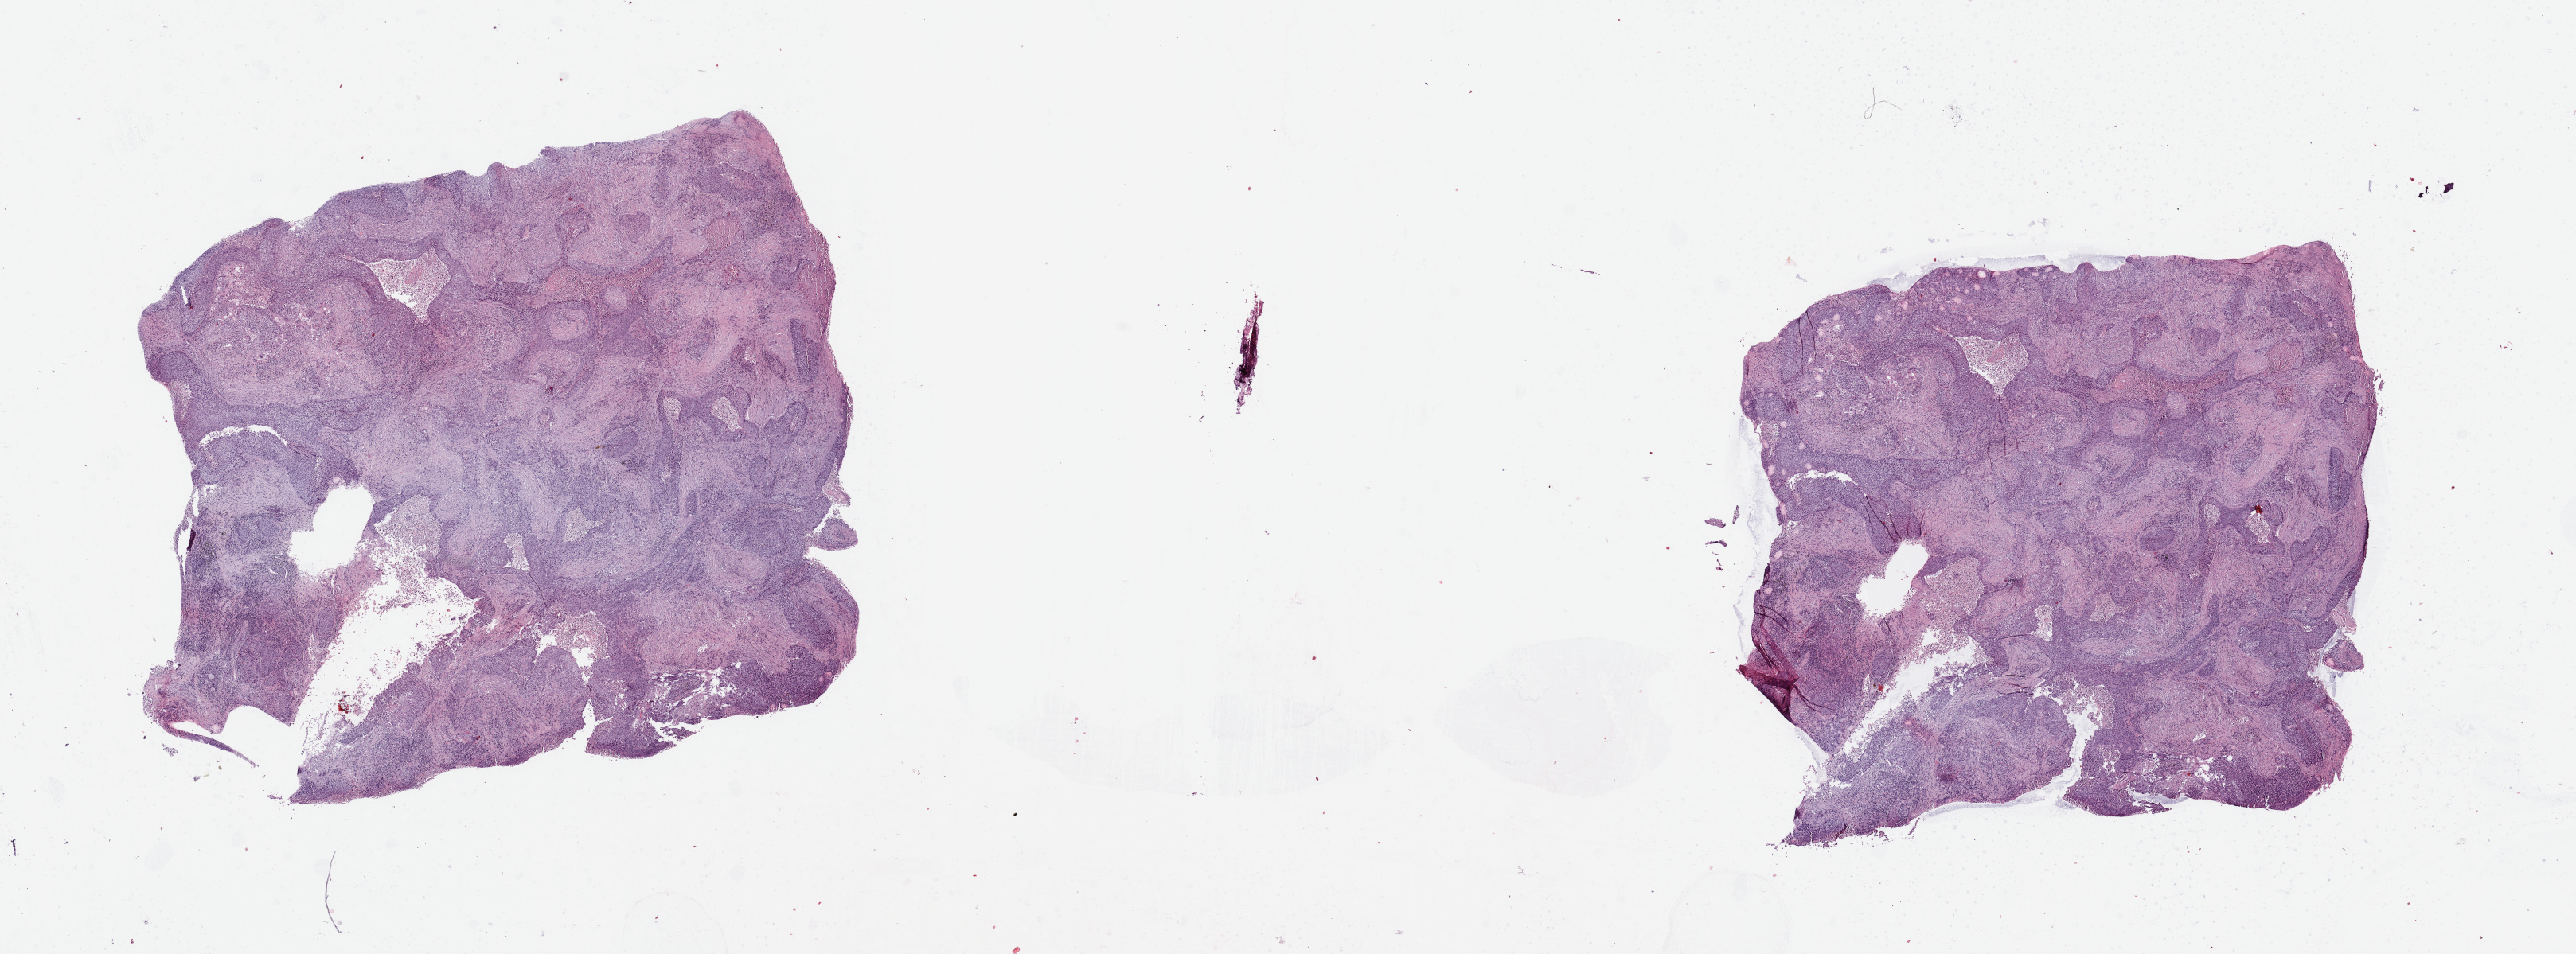
Digitized Hematoxylin and eosin (H&E) stained tissue section (whole slide), a low-resolution overview of the entire scanned area, about 25.6 x 9.5 mm (slide scanned at 20x); tumour tissue sample, lung. 70-year-old male patient.
Histologic diagnosis: Squamous cell carcinoma, NOS.